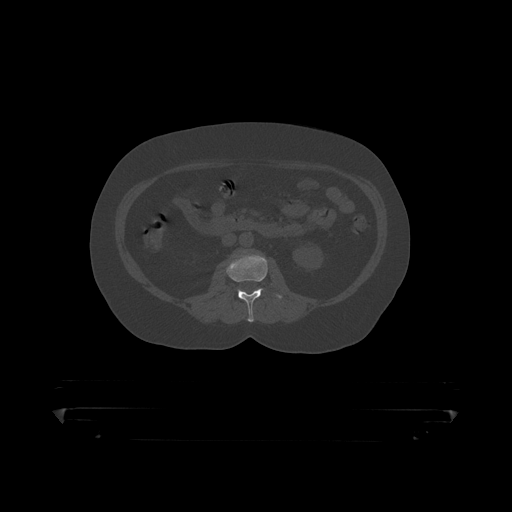
CT including the spine, one axial slice. Position 111 of 390 along the scan axis. Reconstruction kernel STANDARD. 120 kVp. Bone window (W 1800 / L 400 HU). 1.25 mm slice thickness. 512 × 512 image matrix. Male patient, age 60 years. From the clinical record (not read from this slice): primary cancer: prostate.
Outlined on this slice (semi-automatically segmented with operator editing):
- L2 vertebra: bounding box (x1, y1, x2, y2) in pixels: (227, 253, 284, 319)